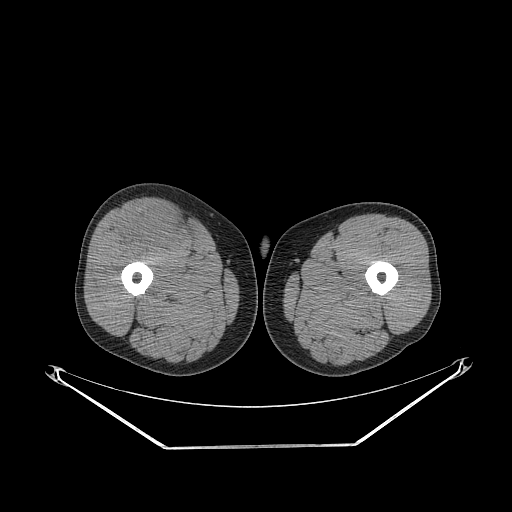
CT of an extremity soft-tissue mass (from a PET/CT study), one axial slice. Position 269 of 311 along the scan axis. 140 kVp. Soft-tissue window (W 400 / L 40 HU). 512 × 512 image matrix, field of view 500 × 500 mm. Male patient. From the clinical record (not read from this slice): histological type: pleiomorphic leiomyosarcoma; grade: intermediate; site of the primary tumour: right thigh.
Outlined on this slice (expert contour drawn on MRI and transferred to this co-registered scan by the dataset authors):
- gross tumour volume including surrounding oedema: bounding box (x1, y1, x2, y2) in pixels: (123, 205, 181, 252)
- gross tumour volume (mass): (123, 206, 181, 250)